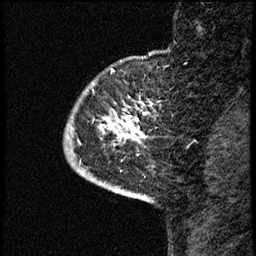
Breast MRI (dynamic contrast-enhanced), one sagittal slice. Position 9 of 68 along the scan axis. Dynamic contrast-enhanced study with each time point stored as its own series, time point 2 of 3 at this slice position (early post-contrast, ordered by acquisition time). 1.5 T. TE 4.2 ms, TR 17.6 ms. 2 mm slice thickness. 256 × 256 image matrix. Female patient, age 52 years. From the clinical record (not read from this slice): setting: breast cancer imaged before/during neoadjuvant chemotherapy; receptor status: HER2-positive.
Annotated regions visible in this slice (semi-automatically segmented with operator editing):
- analysis volume of interest (the breast-tissue region the enhancement analysis was run in; not a lesion): bounding box [x1, y1, x2, y2] px = [64, 61, 171, 184]
- tumour enhancement mask (voxels above the 100 % enhancement threshold inside the analysis volume of interest): [104, 109, 143, 140]